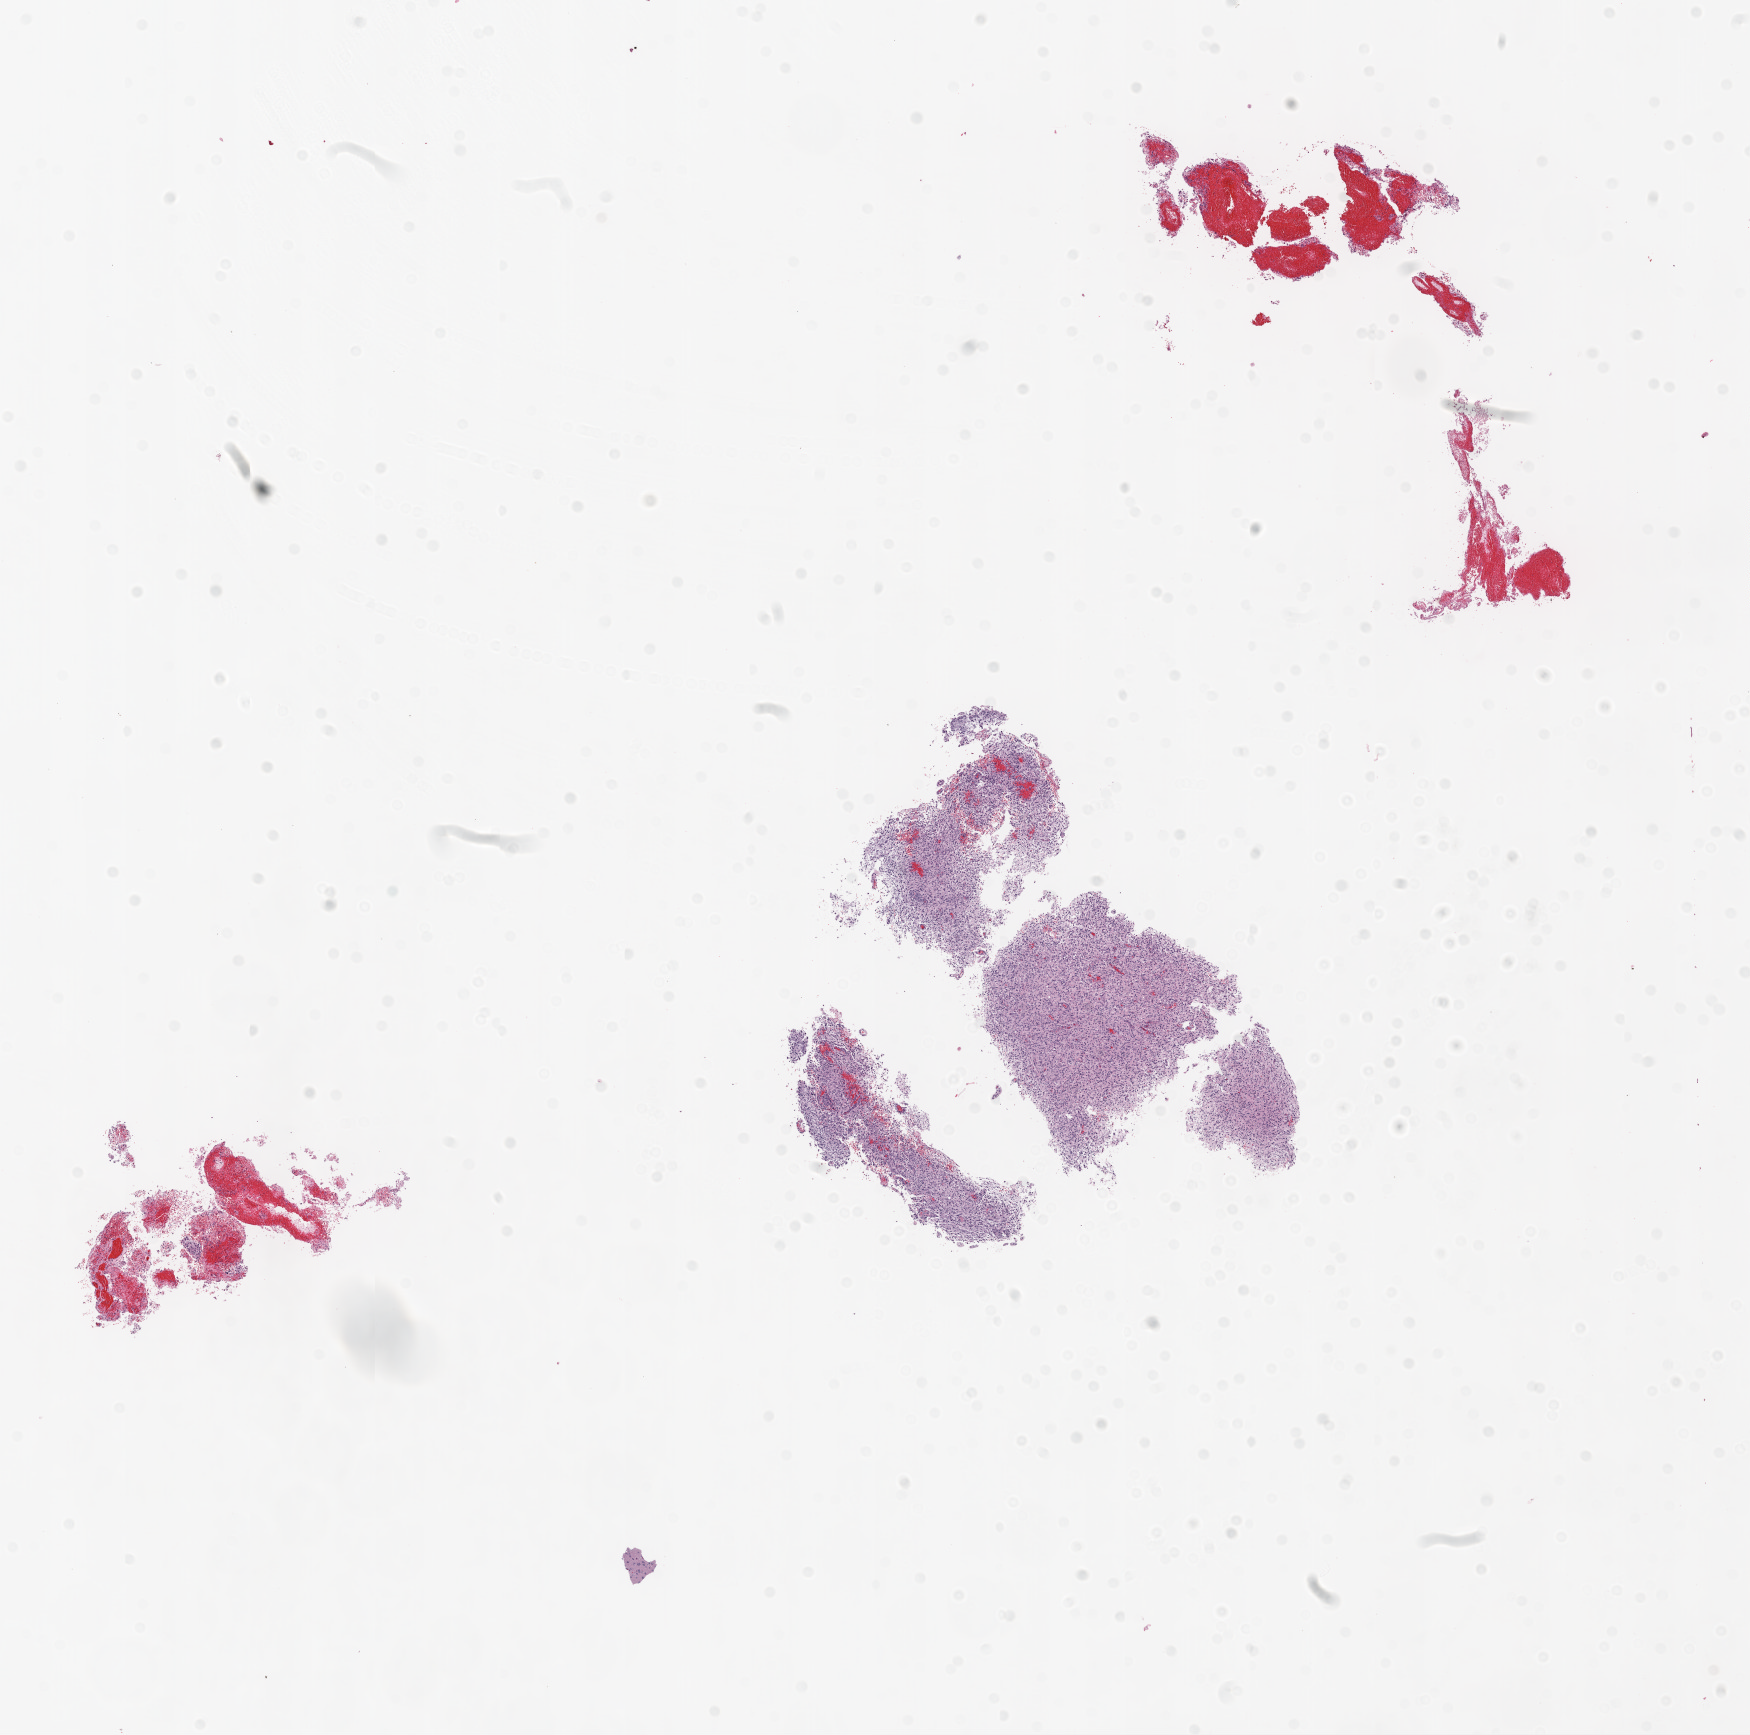
Digitized H&E tissue section (whole slide), whole scanned area (about 14.0 x 13.9 mm) shown as a low-resolution overview, formalin-fixed paraffin-embedded (FFPE) diagnostic section, brain, primary tumour sample. Male, age 30 years at initial diagnosis.
Diagnosis: Glioblastoma.